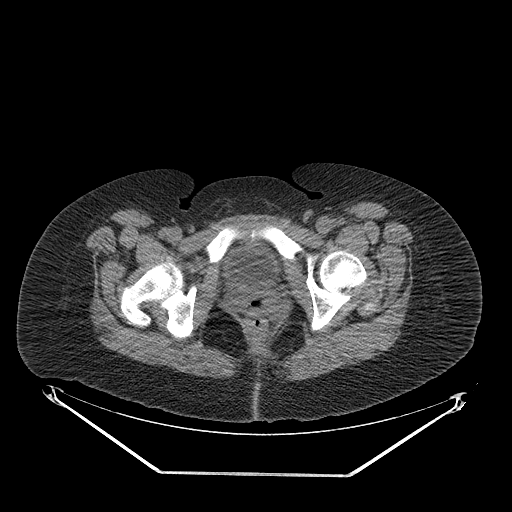
CT of an extremity soft-tissue mass (from a PET/CT study), one axial slice; slice 56 of 267 in the series (ordered by position); 140 kVp; soft-tissue window (W 400 / L 40 HU); 3.75 mm slice thickness; 512 × 512 image matrix, field of view 500 × 500 mm. Female patient. Case-level facts recorded for this patient, not image findings: histological type: myxofibrosarcoma; grade: intermediate; site of the primary tumour: left thigh.
Outlined on this slice (expert contour drawn on MRI and transferred to this co-registered scan by the dataset authors):
- gross tumour volume including surrounding oedema: bounding box (x1, y1, x2, y2) in pixels: (278, 224, 353, 250)